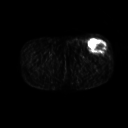
FDG PET of an extremity soft-tissue mass (from a PET/CT study), one axial slice; position 233 of 267 along the scan axis; 128 × 128 image matrix, field of view 500 × 500 mm. Patient: male, 64 years. From the clinical record (not read from this slice): histological type: extraskeletal osteosarcoma; grade: high; site of the primary tumour: thigh.
Structures marked on this image (expert contour drawn on MRI and transferred to this co-registered scan by the dataset authors):
- gross tumour volume (mass): bounding box <88,40,108,53> (left, top, right, bottom; pixels)